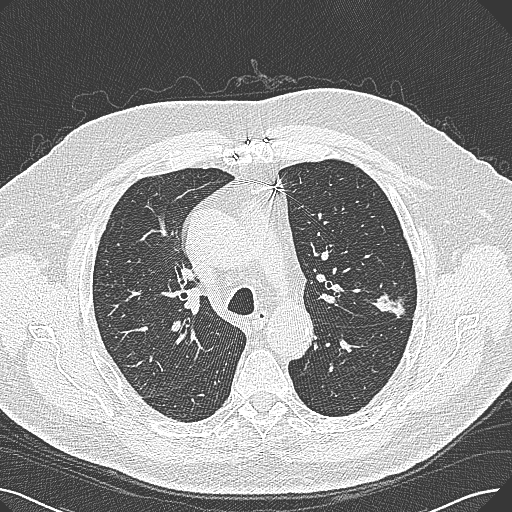
Axial slice from a low-dose chest CT screening exam; baseline annual screen; lung window (W 1500 / L -600 HU); 120 kVp. Male, age 74 years at enrolment. Former smoker at enrolment.
Lesion marked by an expert reader, box from (x=366, y=273) to (x=427, y=325) px. Reader record for this screening exam (exam-level; its link to the box is not recorded): non-calcified nodule or mass ≥4 mm, left upper lobe, 15 × 10 mm, poorly defined margins, soft tissue attenuation. Official screen result: positive, change unspecified: nodule(s) >= 4 mm or enlarging nodule(s), mass(es), or other non-specific abnormalities suspicious for lung cancer. Later outcome: lung cancer diagnosed 124 days after this screen — adenocarcinoma, NOS, left upper lobe, well differentiated (G1), stage IA (AJCC 6th edition), 26 mm at pathology.